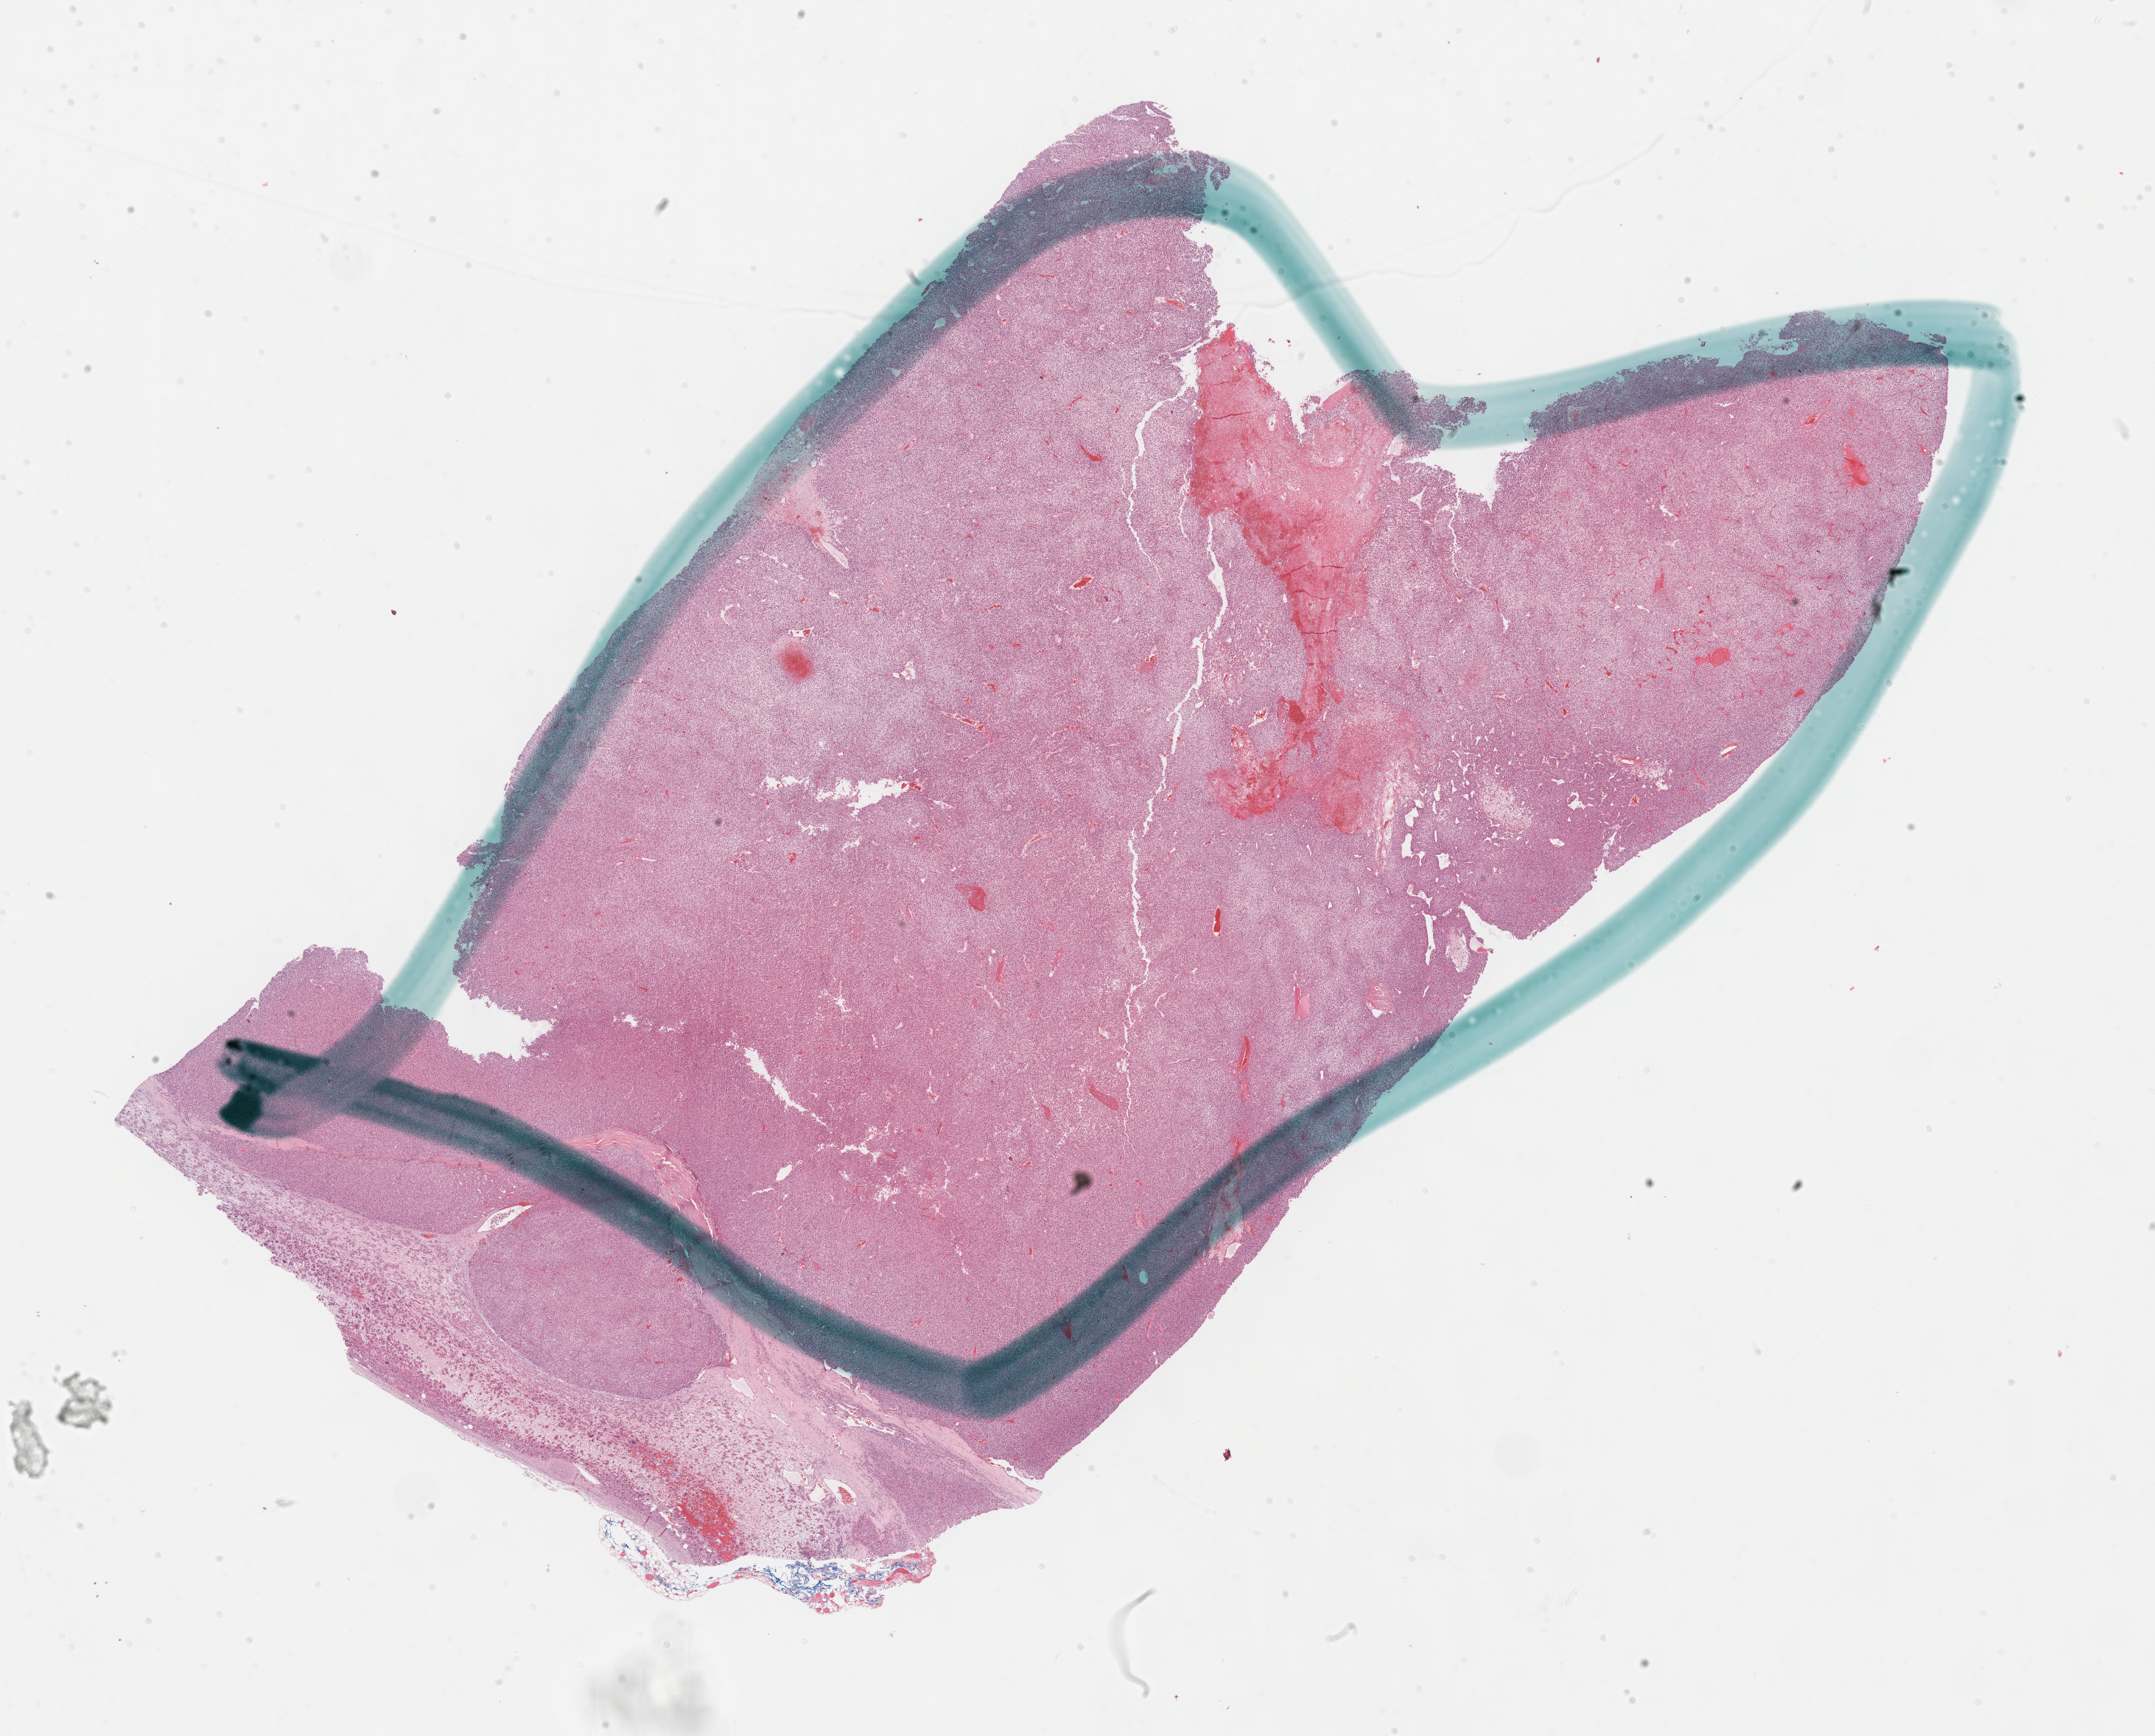
Hematoxylin and eosin (H&E) stained whole-slide image — low-resolution overview of the scanned area, about 23.7 x 19.1 mm, formalin-fixed paraffin-embedded (FFPE) diagnostic section, adrenal cortex, primary tumour sample. Male, age 60 years at initial diagnosis.
- diagnosis: Adrenal cortical carcinoma (cortex of adrenal gland)